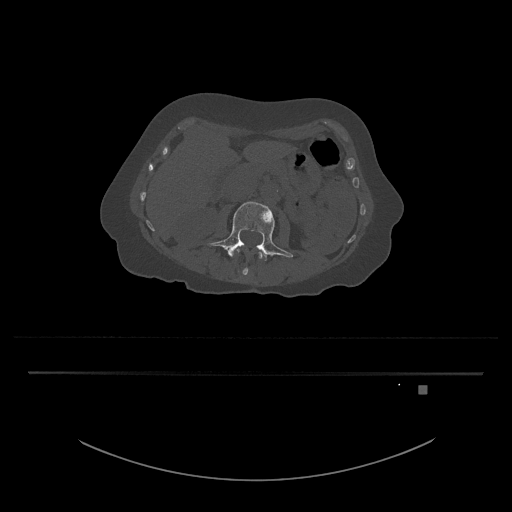
CT including the spine, one axial slice; slice 439 of 797 in the series (ordered by position); bone window (W 1800 / L 400 HU); 0.5 mm slice thickness; 512 × 512 image matrix. Female patient, age 57 years. Case-level facts recorded for this patient, not image findings: primary cancer: cervical.
Structures marked on this image (semi-automatic segmentation, software-assisted and operator-edited):
- L3 vertebra: bounding box [x1, y1, x2, y2] px = [207, 201, 293, 261]